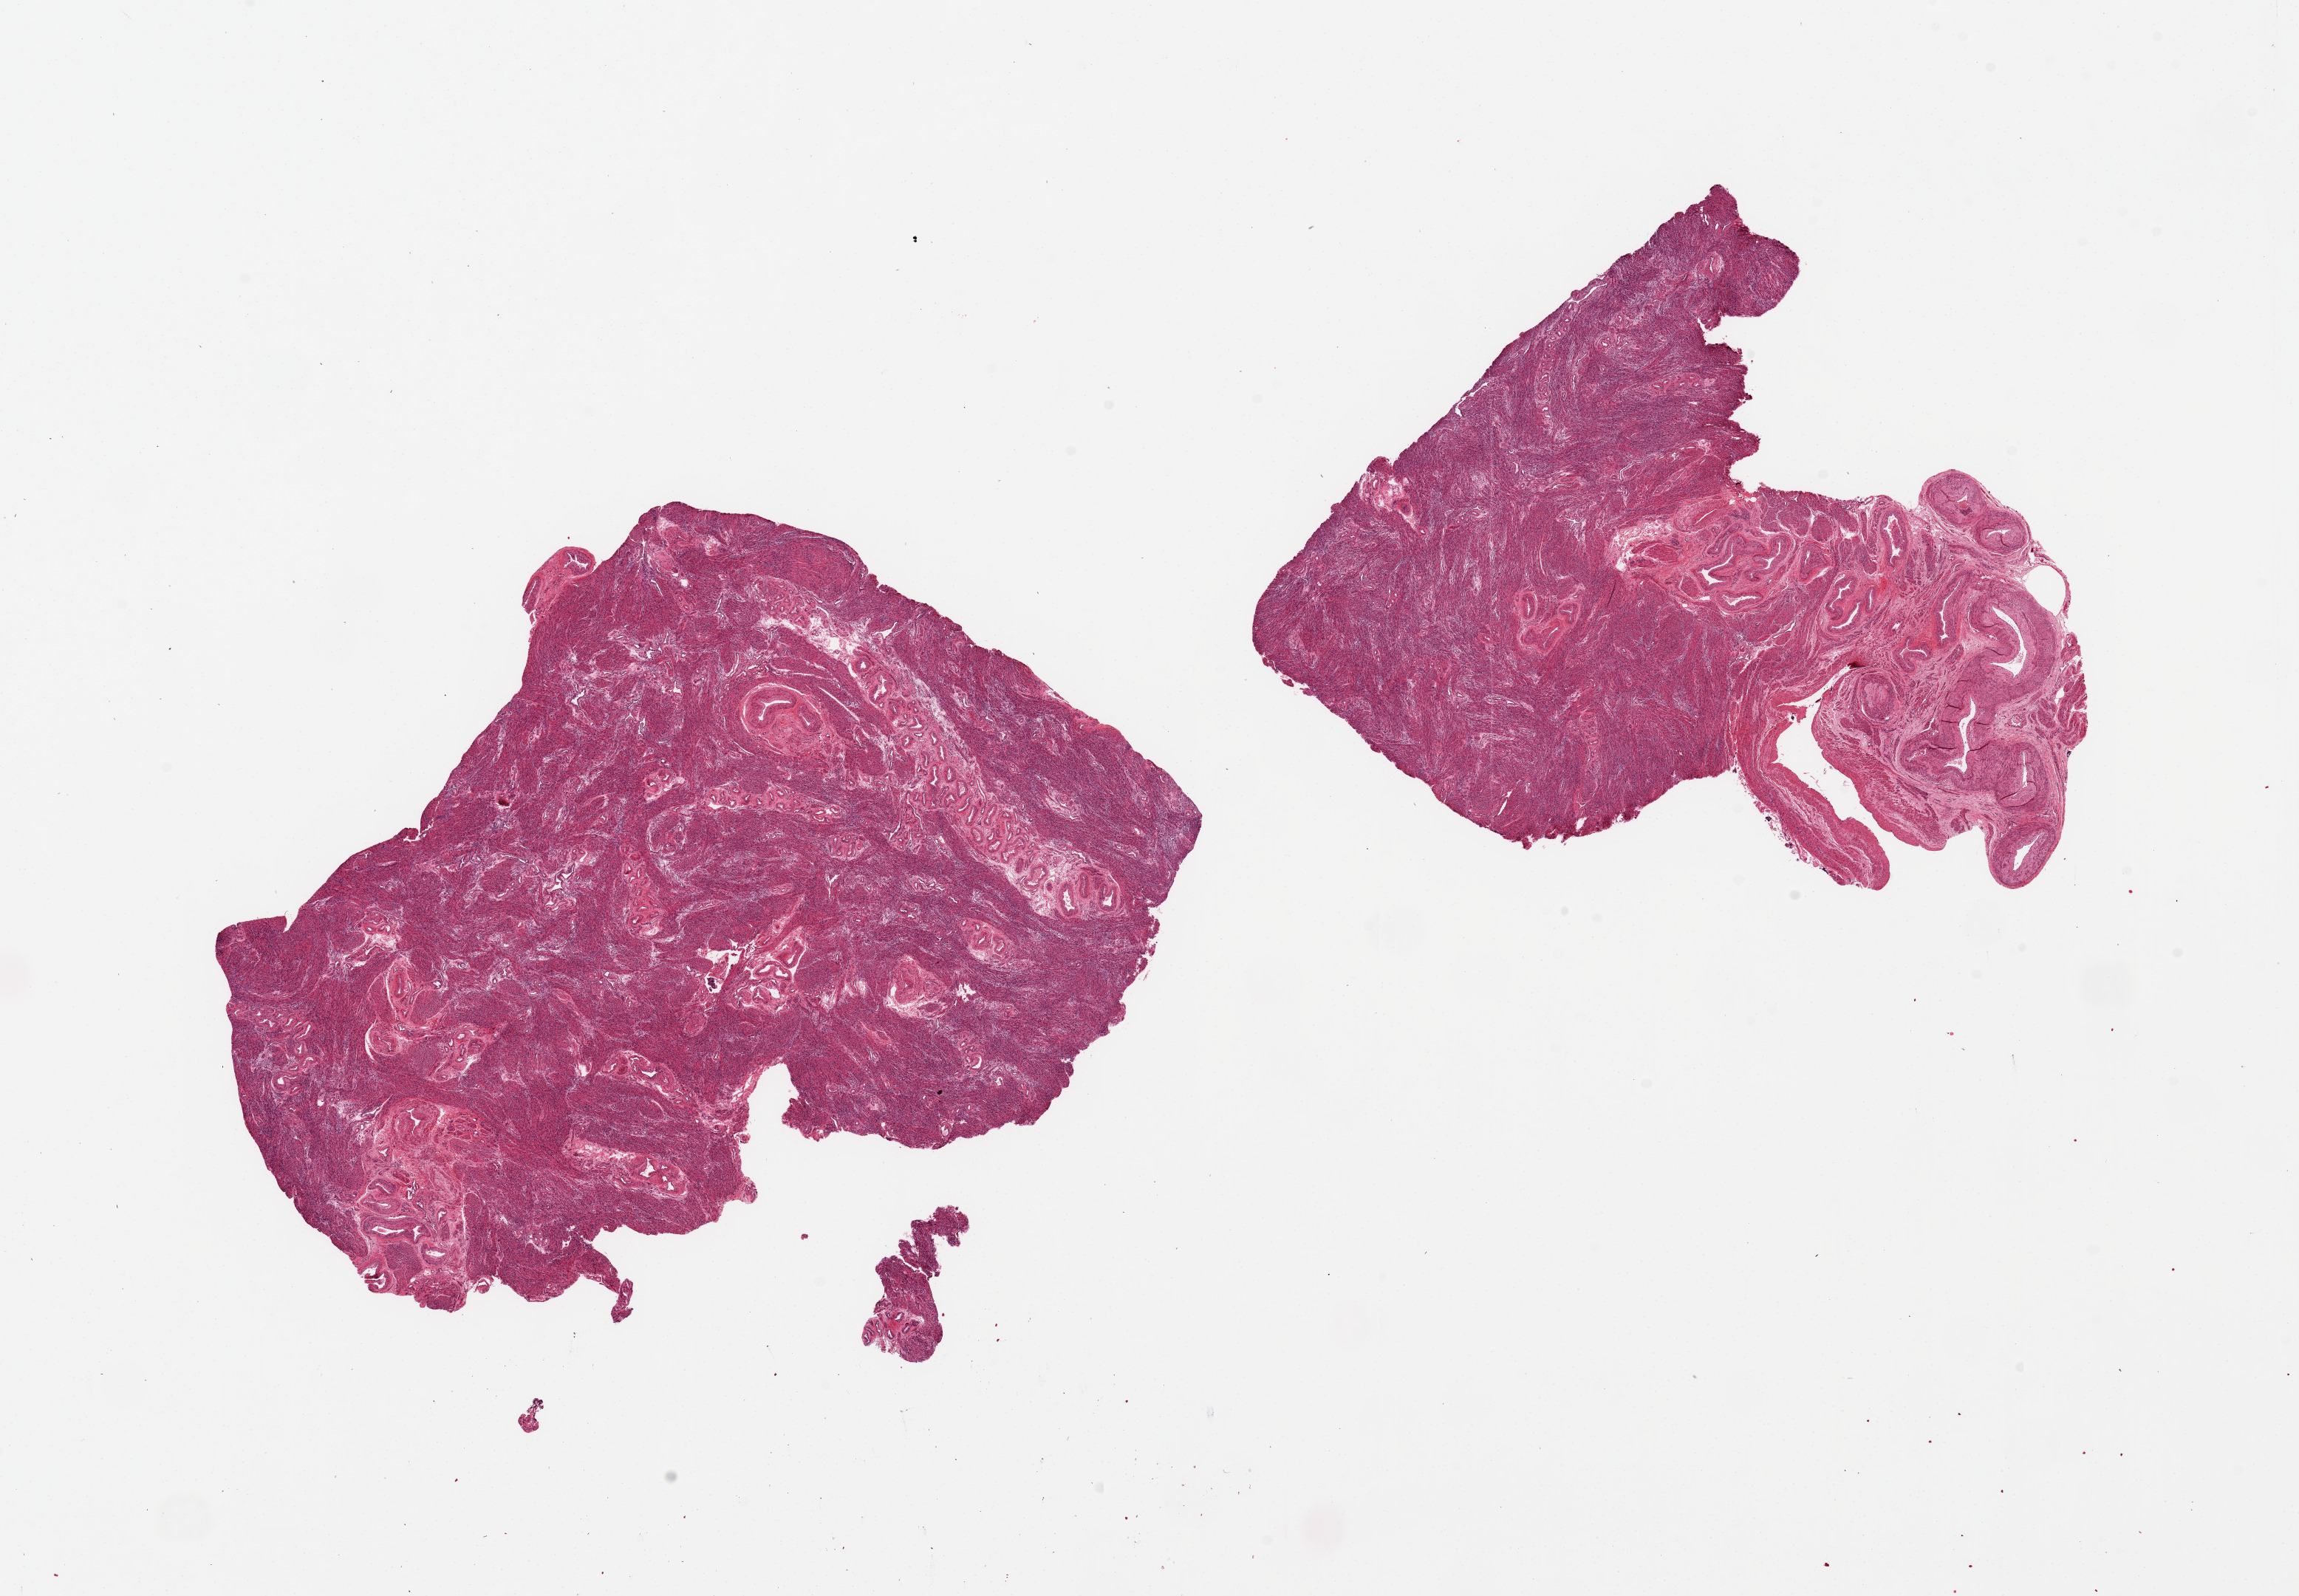
Digitized hematoxylin and eosin (H&E)-stained section, brightfield, low-resolution overview of the scanned area, about 24.6 x 17.1 mm (slide scanned at 20x), PAXgene-fixed paraffin-embedded (PFPE) section, target tissue: uterus, tissue donor sample. Donor: female.
Pathologist's review note for this sample: 2 pieces, 8x8 & 8x7mm; all myometrium, no endometrium in these sections.